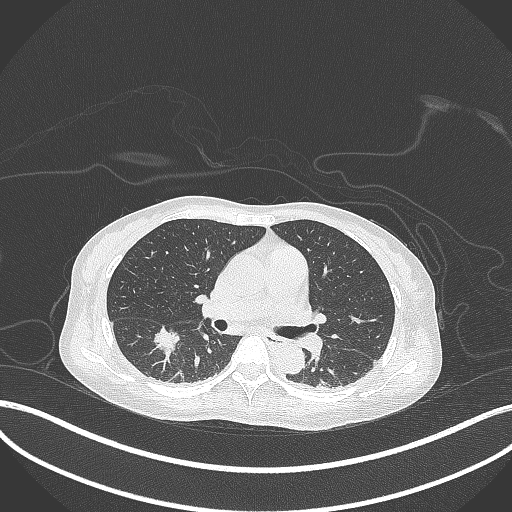
Chest CT, one axial slice; slice 174 of 261 in the series (ordered by position); reconstruction kernel B70f; 120 kVp; lung window (W 1500 / L -600 HU); 1 mm slice thickness; 512 × 512 image matrix, field of view 400 × 400 mm. Patient: female, 44 years. From the clinical record (not read from this slice): clinical TNM (as recorded): T1c N0 M0.
Outlined on this slice (rectangle marked by the reading radiologist):
- lung tumour (recorded histology: adenocarcinoma): bounding box <151,325,180,359> (left, top, right, bottom; pixels)